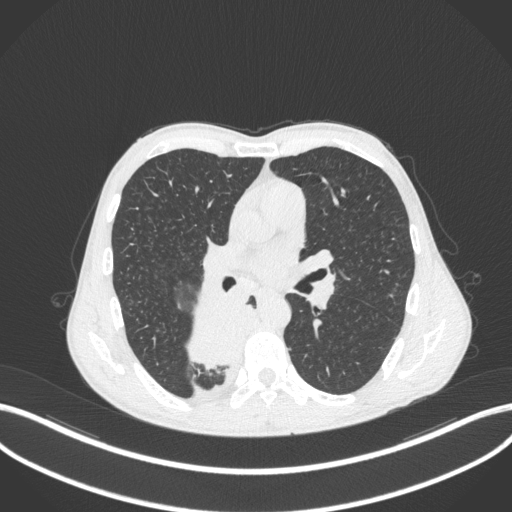
Chest CT, one axial slice. Slice 208 of 371 in the series (ordered by position). Reconstruction kernel B31f. 120 kVp. Lung window (W 1500 / L -600 HU). 1 mm slice thickness. 512 × 512 image matrix. Male patient, age 58 years. Case-level facts recorded for this patient, not image findings: clinical TNM (as recorded): T3 N1 M1.
Outlined on this slice (rectangle marked by the reading radiologist):
- lung tumour (recorded histology: squamous cell carcinoma): bounding box [x1, y1, x2, y2] px = [178, 290, 269, 370]